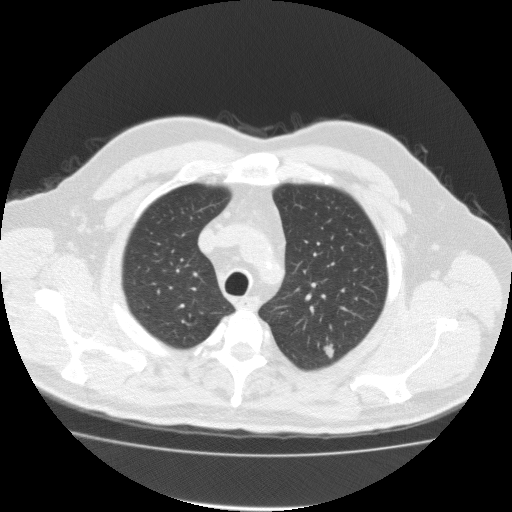
Chest CT (low-dose screening protocol), one axial image; baseline annual screen; lung window (W 1500 / L -600 HU); 2 mm slice thickness; 120 kVp; slice 27 of 161 in the series; 512 × 512 image matrix. Male, age 57 years at enrolment. Former smoker at enrolment.
• Expert-annotated lung lesion, box from (x=318, y=336) to (x=350, y=370) px.
• Screening reader's record for this exam (one nodule recorded; not confirmed to be the boxed lesion): non-calcified nodule or mass ≥4 mm, left upper lobe, 11 × 8 mm, spiculated (stellate) margins, soft tissue attenuation.
• Participant outcome: lung cancer diagnosed 19 days after this screen — bronchiolo-alveolar adenocarcinoma, NOS, left upper lobe, well differentiated (G1), stage IA (AJCC 6th edition), 80 mm at pathology.